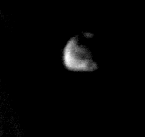
Cropped region of a digitized screen-film mammogram centred on a radiologist-marked abnormality; left breast; MLO view; BI-RADS breast density category 1 (scale 1–4).
Calcifications, morphology lucent center; BI-RADS assessment category 2; subtlety rating 5 on a 1 (subtle) to 5 (obvious) scale; benign without callback (not worked up further).